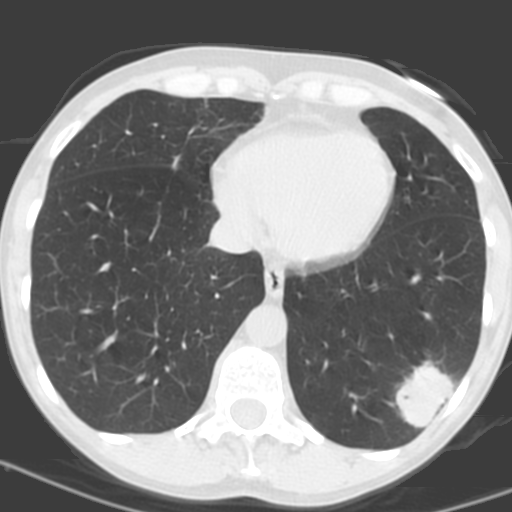
Low-dose screening chest CT, one axial slice; position 49 of 156 along the scan axis; 120 kVp; lung window (W 1500 / L -600 HU); 3.2 mm slice thickness; 512 × 512 image matrix, field of view 262 × 262 mm.
Structures marked on this image (expert manual segmentation):
- lesion 1 (tumor, lower lobe of left lung): box from (x=394, y=360) to (x=454, y=428) px